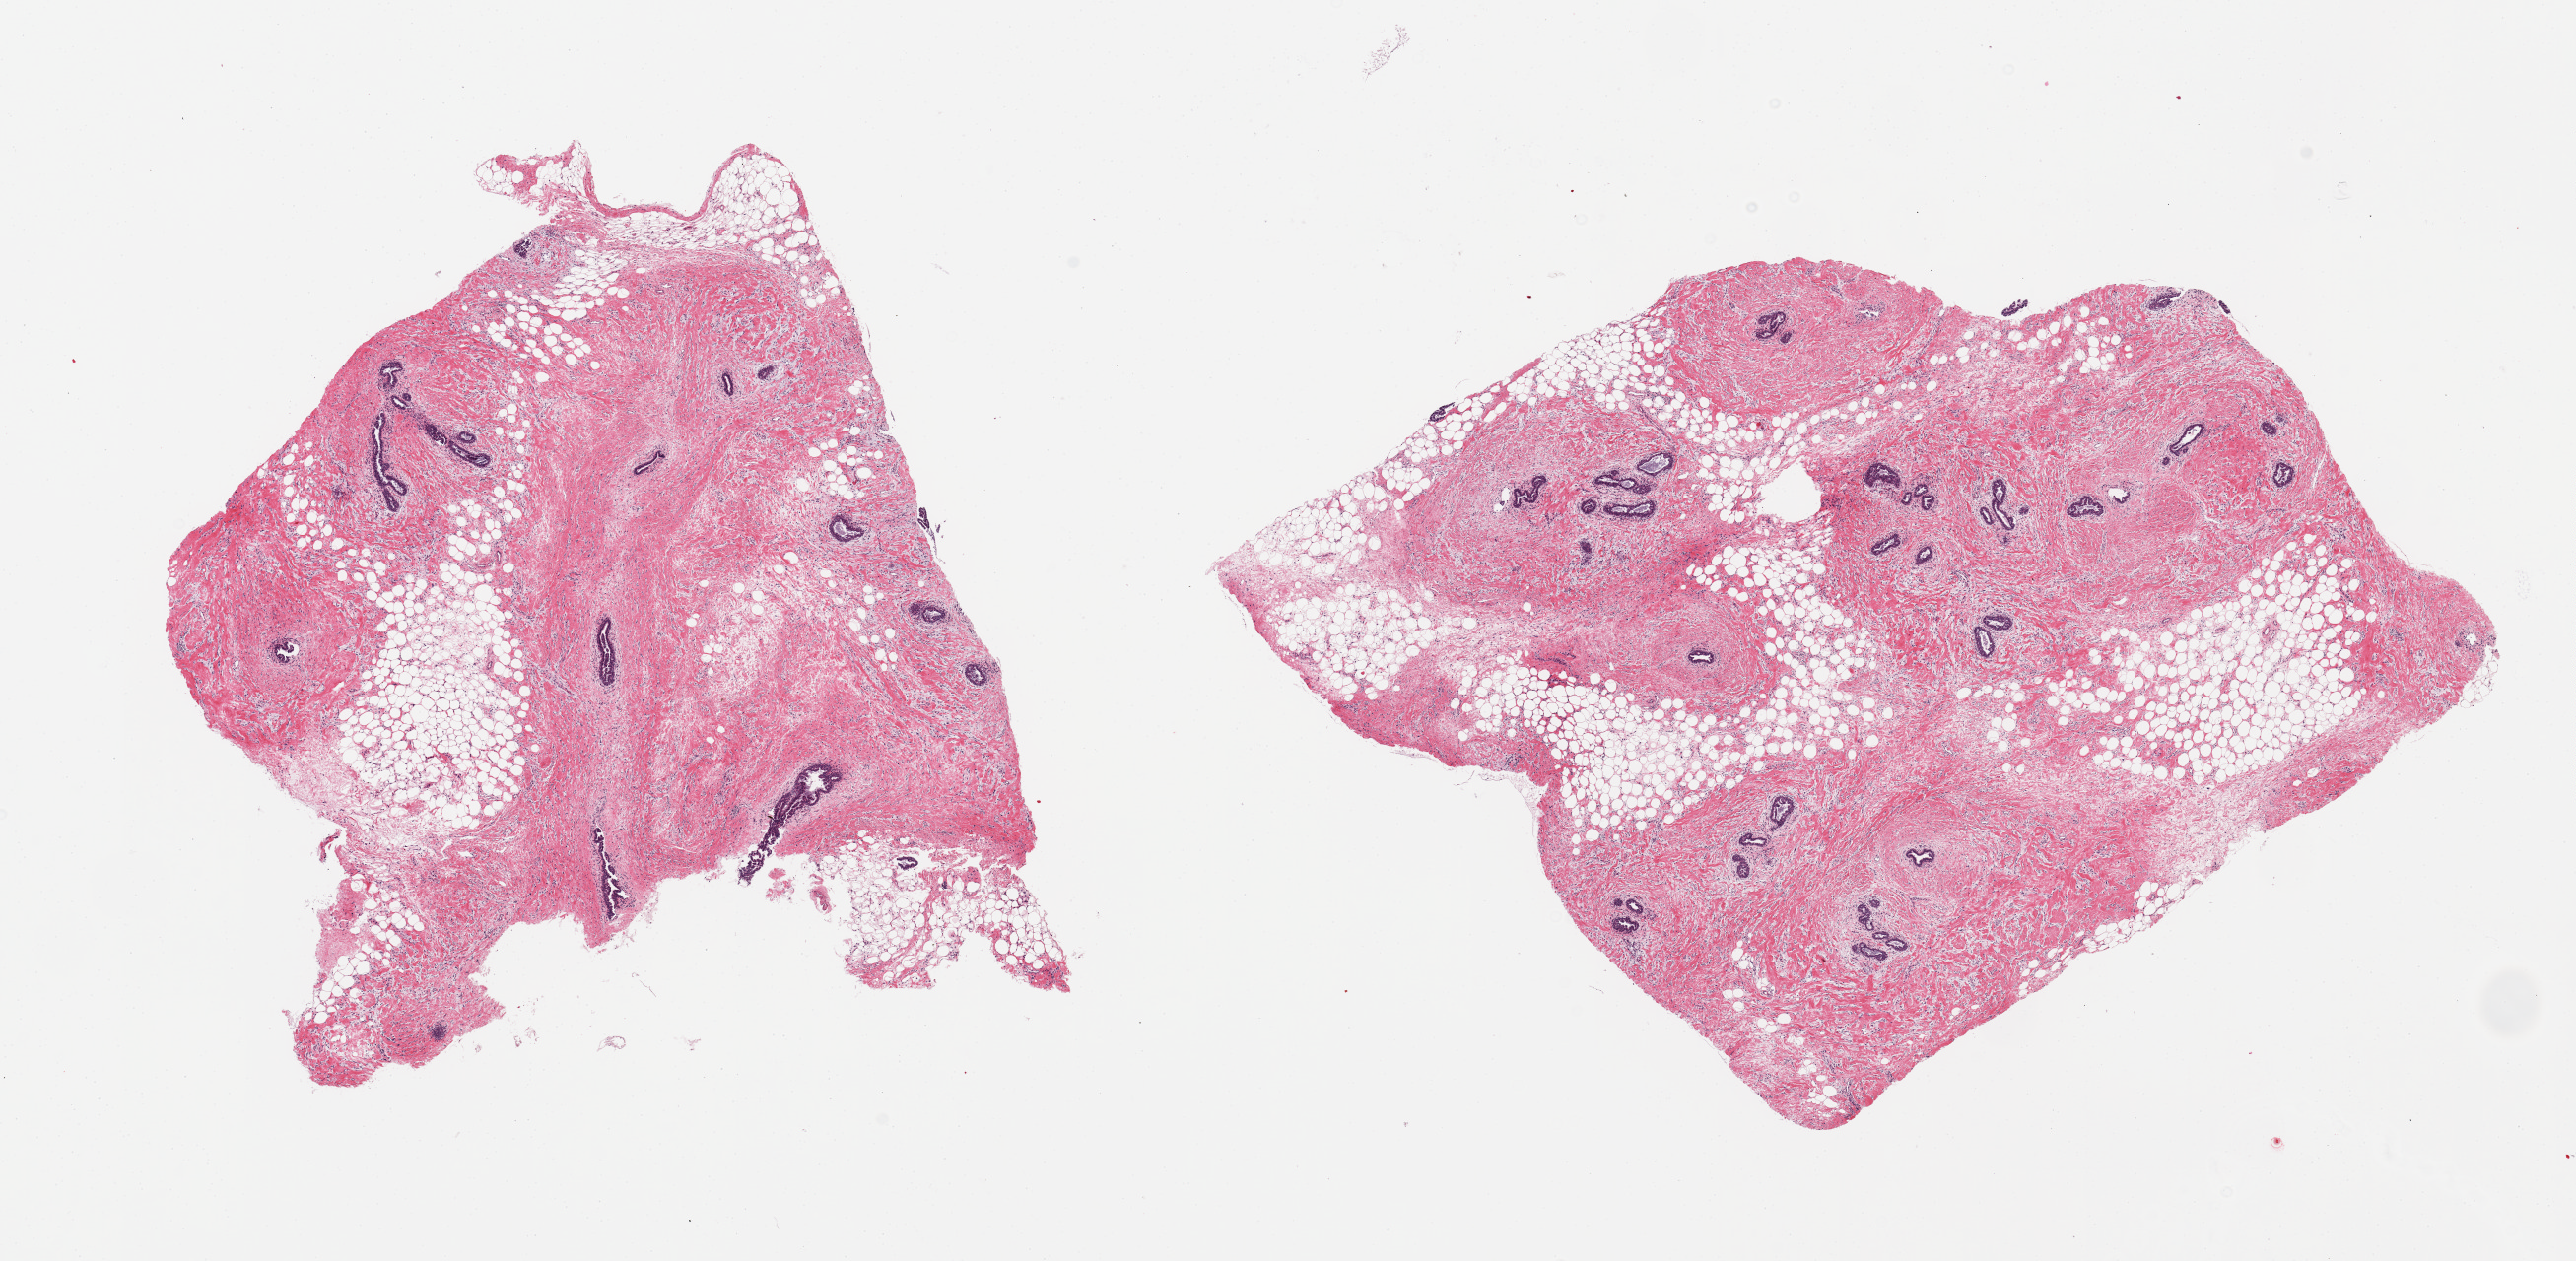
Digitized H&E-stained section, brightfield — low-resolution overview of the scanned area, about 20.7 x 10.1 mm (from a 20x scan); PAXgene-fixed paraffin-embedded (PFPE) section; section of breast (target tissue); donor tissue sample. Donor sex: male.
Pathologist's review note for this sample: 2 pieces; prominent ducts and fibrosis of gynecomastia.